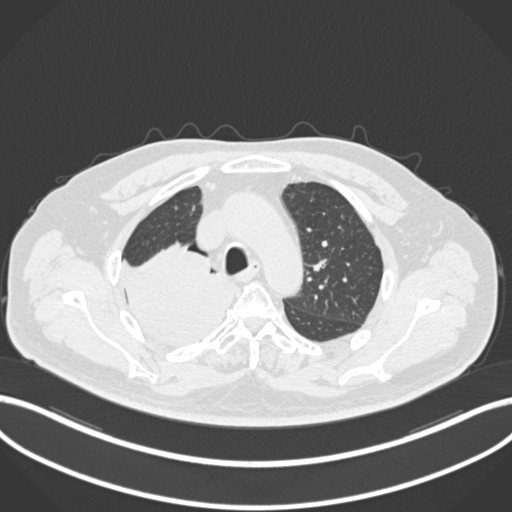
Chest CT, one axial slice; reconstruction kernel B30f; 120 kVp; lung window (W 1500 / L -600 HU); 1 mm slice thickness; 512 × 512 image matrix, field of view 400 × 400 mm. Patient: male, 68 years. Case-level facts recorded for this patient, not image findings: clinical TNM (as recorded): T2a N0 M0.
Structures marked on this image (bounding box drawn by a radiologist):
- lung tumour (recorded histology: adenocarcinoma): box from (x=119, y=246) to (x=238, y=344) px